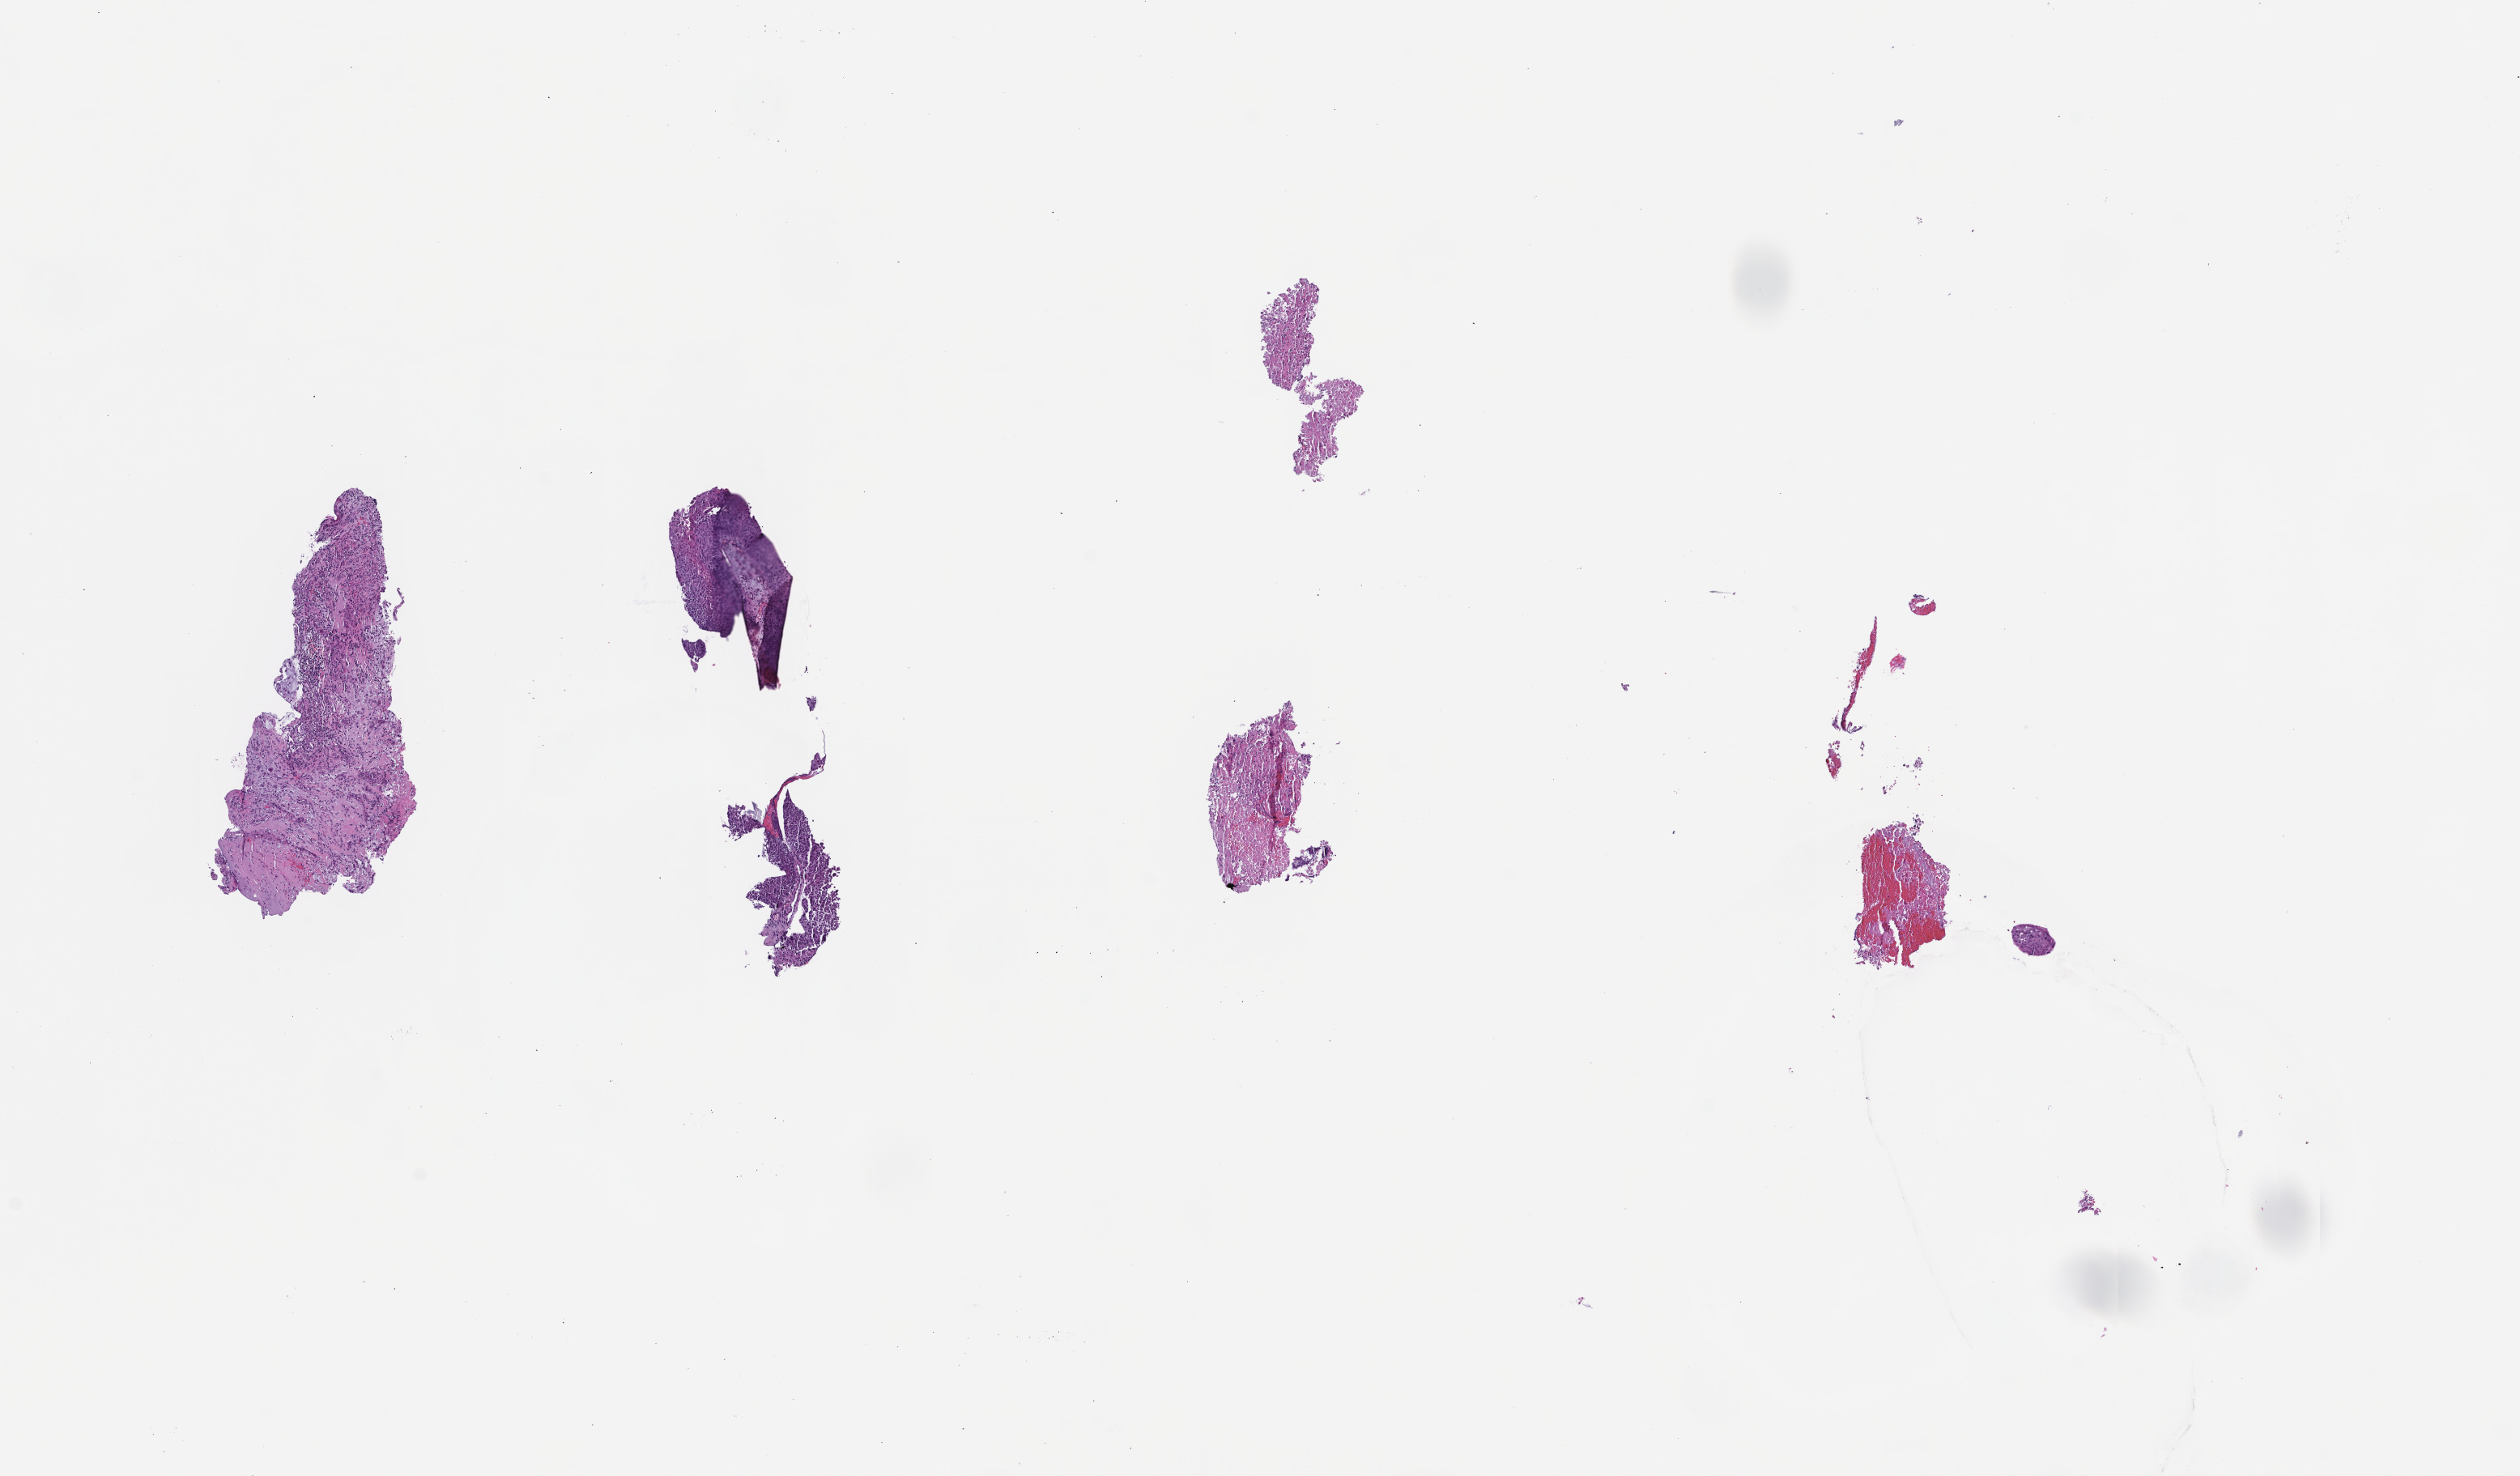
Digitized H&E-stained section — whole scanned area (about 12.6 x 7.4 mm) shown as a low-resolution overview; formalin-fixed paraffin-embedded section; archival tissue. Patient: male.
* this section: metastatic tumor tissue
* primary diagnosis of the patient: Non-Small Cell Lung Carcinoma